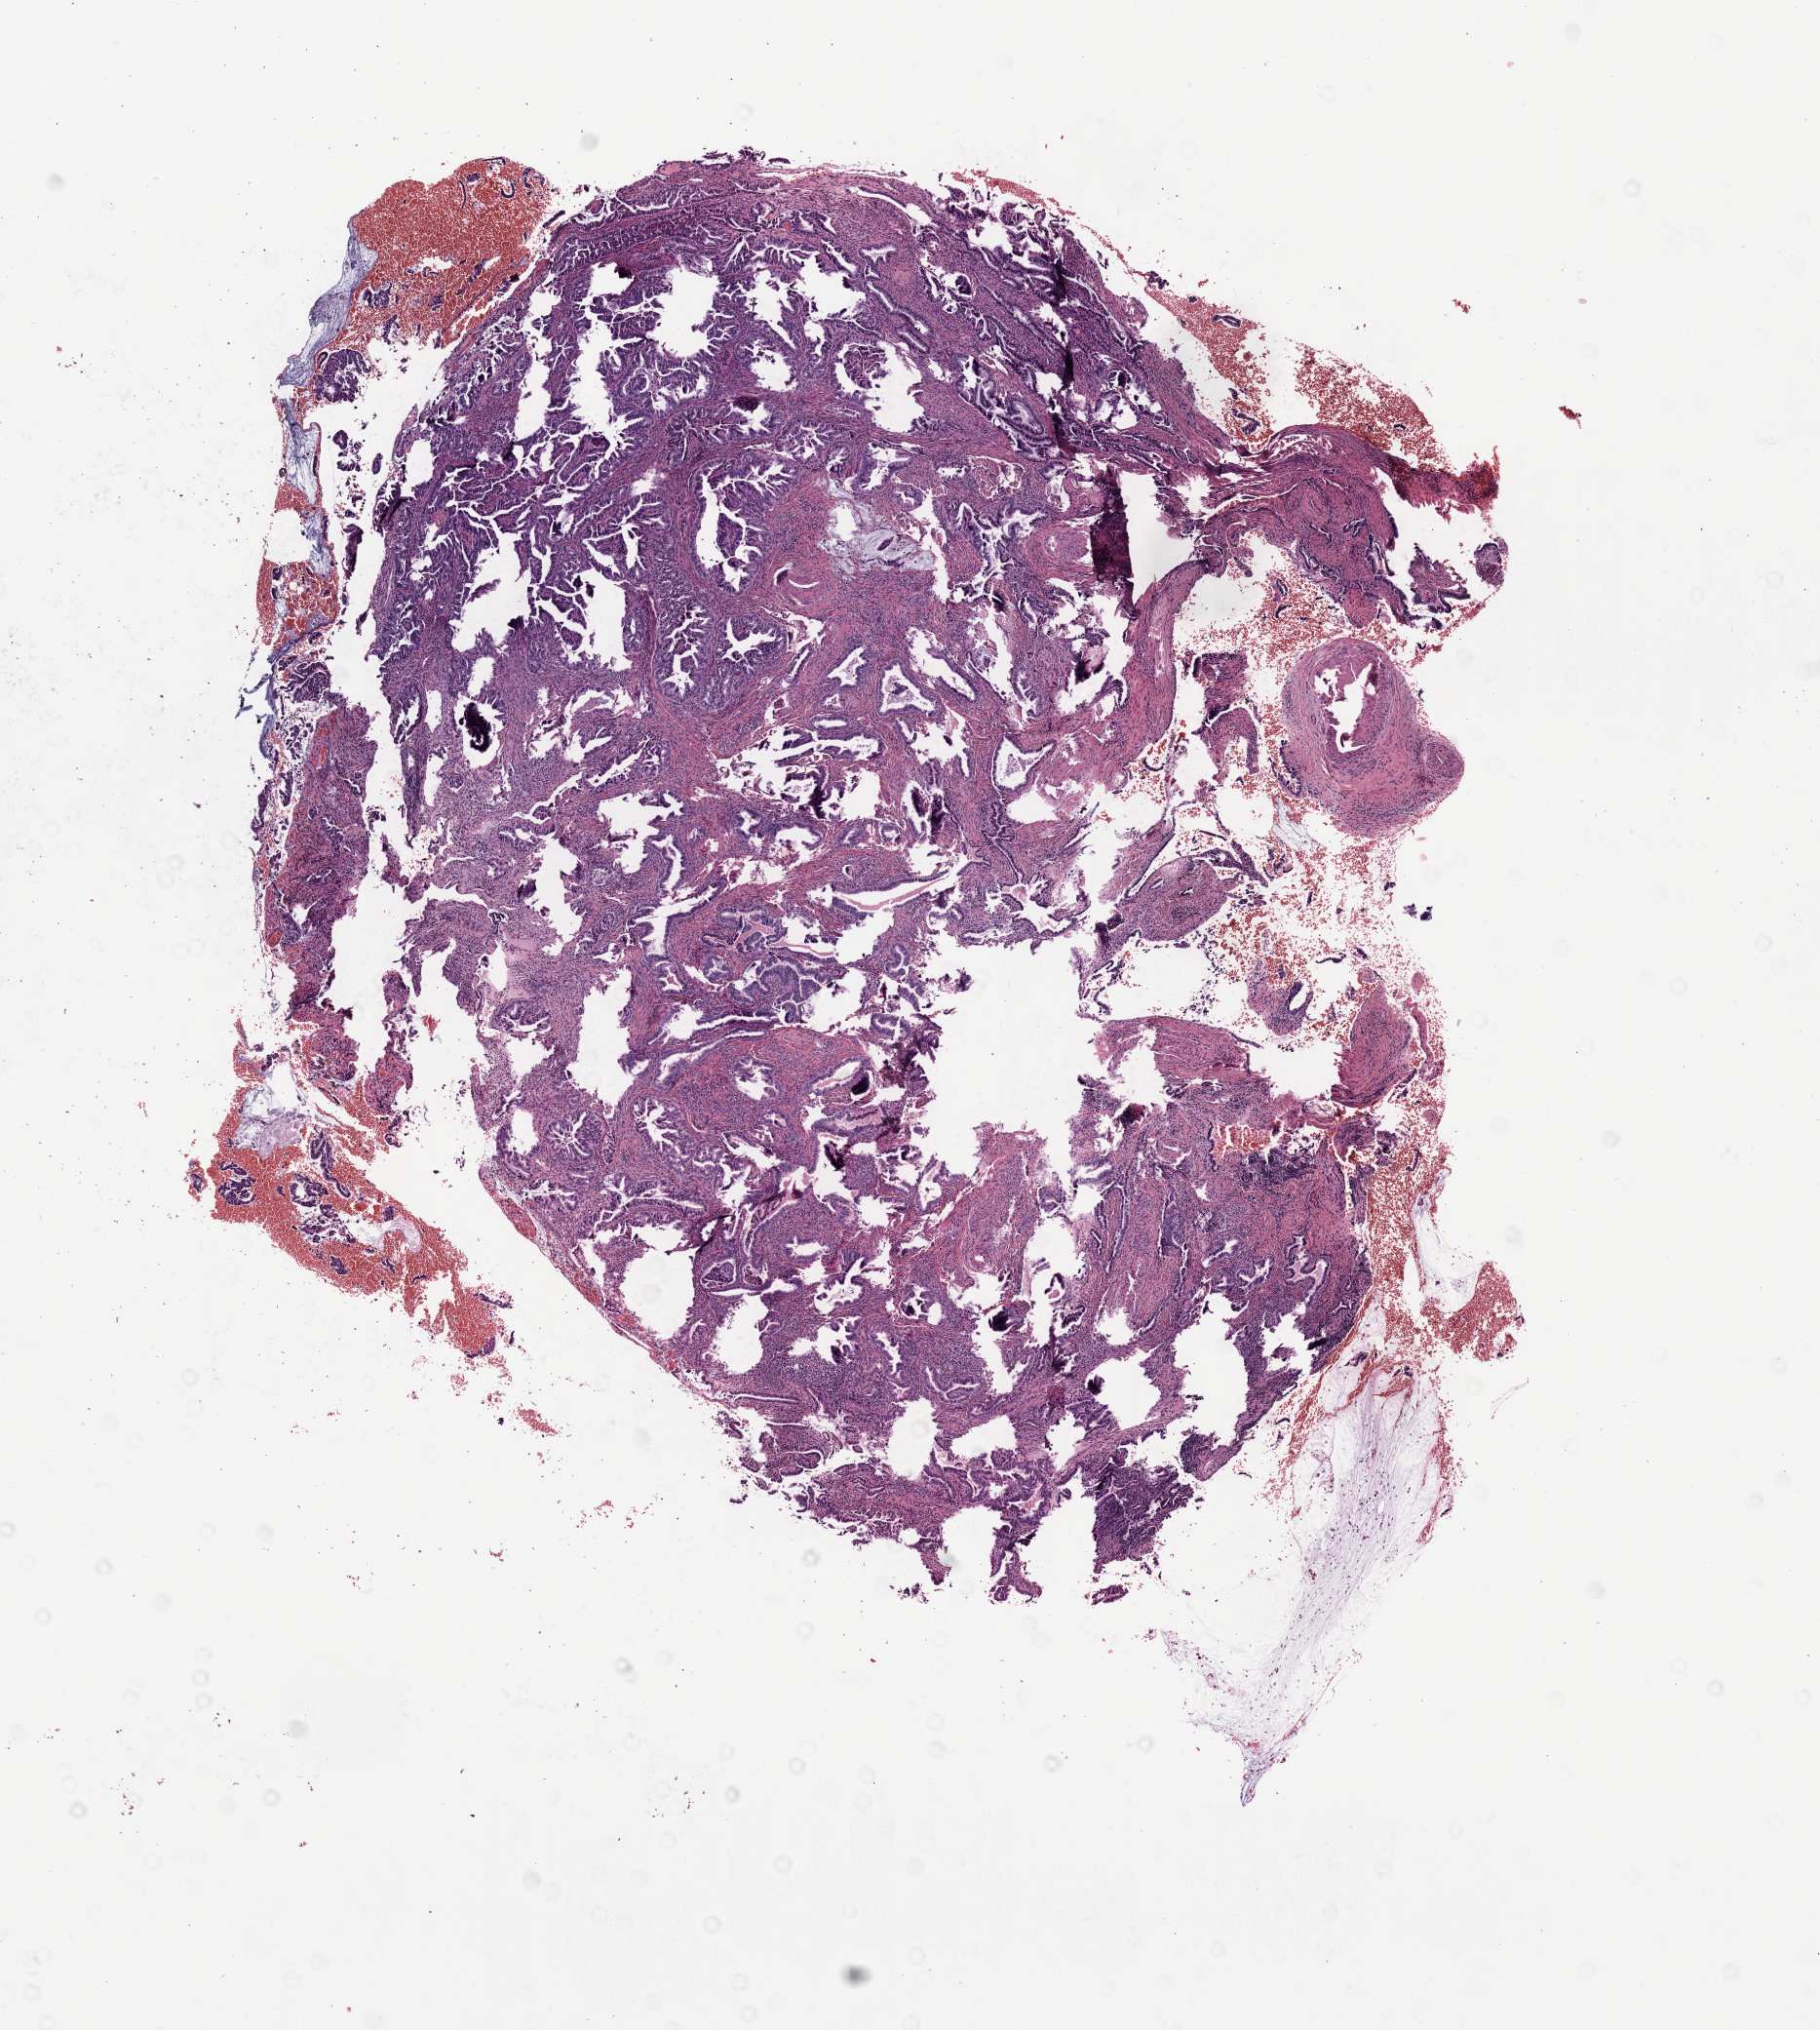
Whole-slide histology image, Hematoxylin and eosin (H&E) stained — low-resolution overview of the scanned area, about 7.6 x 8.4 mm, formalin-fixed paraffin-embedded (FFPE) diagnostic section, sample: primary tumour, cervix. Female patient; age at initial diagnosis 50 years. Histologic grade: G2 (moderately differentiated).
FIGO stage: IIB. Diagnosis: Mucinous adenocarcinoma, endocervical type (cervix uteri).